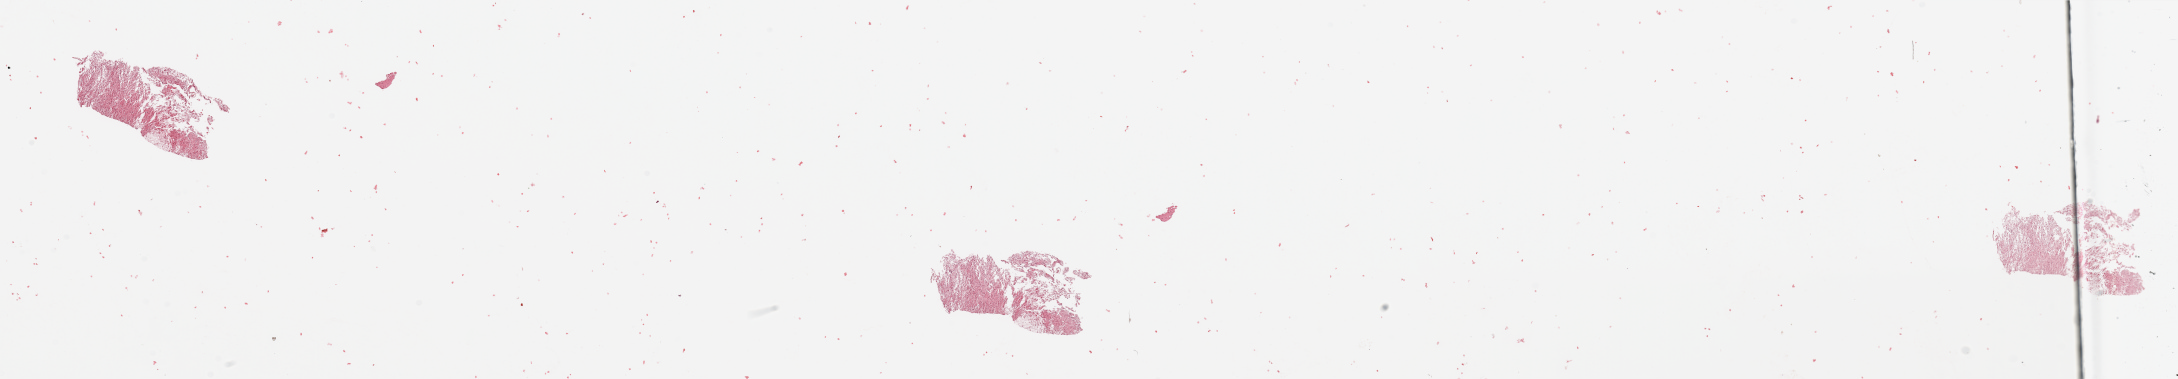
Whole-slide histology image, H&E — low-resolution overview of the scanned area, about 34.5 x 6.0 mm (from a 20x scan). Tumour tissue sample, brain. Male, 62 y/o.
- primary tumour site (as recorded): frontal lobe
- histologic diagnosis: Glioblastoma